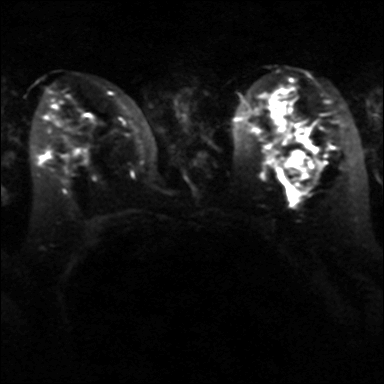
Breast MRI, one axial slice. Position 19 of 40 along the scan axis. Diffusion-weighted series; image 2 of 4 stored at this slice position (different b-values; order by instance number). 3 T. 384 × 384 image matrix, field of view 320 × 320 mm. Female patient.
Structures marked on this image (expert manual segmentation):
- tumour on diffusion-weighted imaging: box from (x=283, y=150) to (x=315, y=181) px